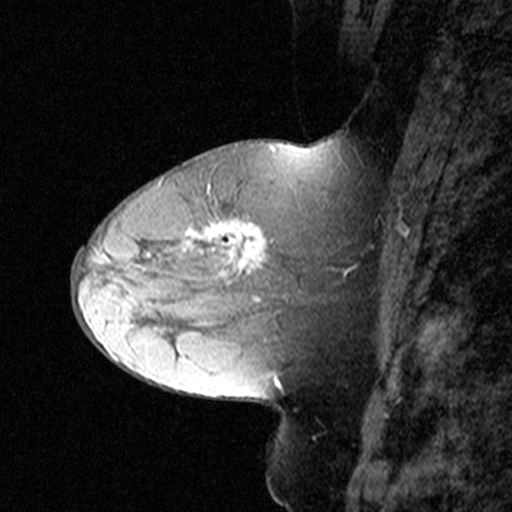
Breast MRI (dynamic contrast-enhanced), one sagittal slice; position 20 of 44 along the scan axis; dynamic contrast-enhanced study with each time point stored as its own series, time point 2 of 3 at this slice position (early post-contrast, ordered by acquisition time); 1.5 T; TE 4.5 ms, TR 11 ms; 3 mm slice thickness; 512 × 512 image matrix, field of view 200 × 200 mm. Female patient, age 50 years. From the clinical record (not read from this slice): setting: breast cancer imaged before/during neoadjuvant chemotherapy; receptor status: HR-positive, HER2-negative.
Outlined on this slice (semi-automatically segmented with operator editing):
- analysis volume of interest (the breast-tissue region the enhancement analysis was run in; not a lesion): bounding box (x1, y1, x2, y2) in pixels: (180, 198, 349, 311)
- tumour enhancement mask (voxels above the 90 % enhancement threshold inside the analysis volume of interest): (184, 219, 347, 301)